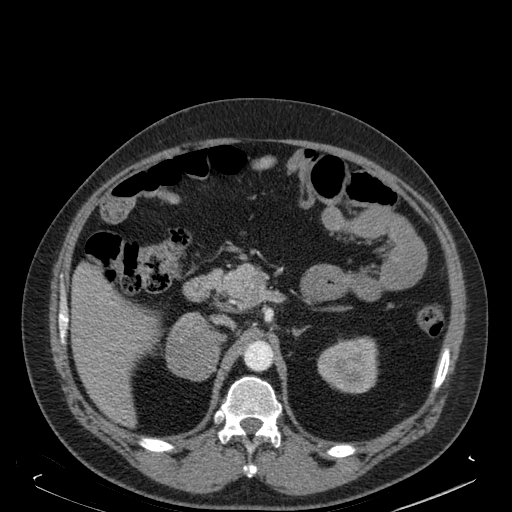
Contrast-enhanced abdominal CT, one axial slice; slice 110 of 181 in the series (ordered by position); soft-tissue window (W 400 / L 40 HU); 512 × 512 image matrix. Male patient. From the clinical record (not read from this slice): diagnosis: adrenocortical carcinoma; tumour side: right adrenal; tumour size at pathology: 7.5 cm.
Outlined on this slice (semi-automatic segmentation, software-assisted and operator-edited):
- mass: bounding box <166,314,219,379> (left, top, right, bottom; pixels)